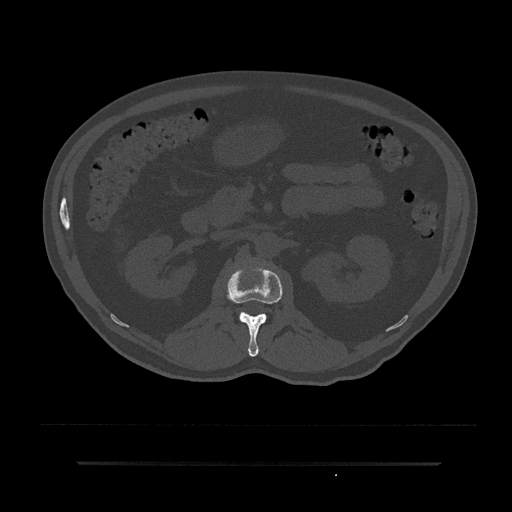
CT including the spine, one axial slice; slice 123 of 797 in the series (ordered by position); reconstruction kernel Br40s/3; 120 kVp; bone window (W 1800 / L 400 HU); 0.5 mm slice thickness; 512 × 512 image matrix. Patient: male, 59 years. Case-level facts recorded for this patient, not image findings: primary cancer: bile ducts.
Annotated regions visible in this slice (semi-automatic segmentation, software-assisted and operator-edited):
- L1 vertebra: bounding box <225,266,283,357> (left, top, right, bottom; pixels)